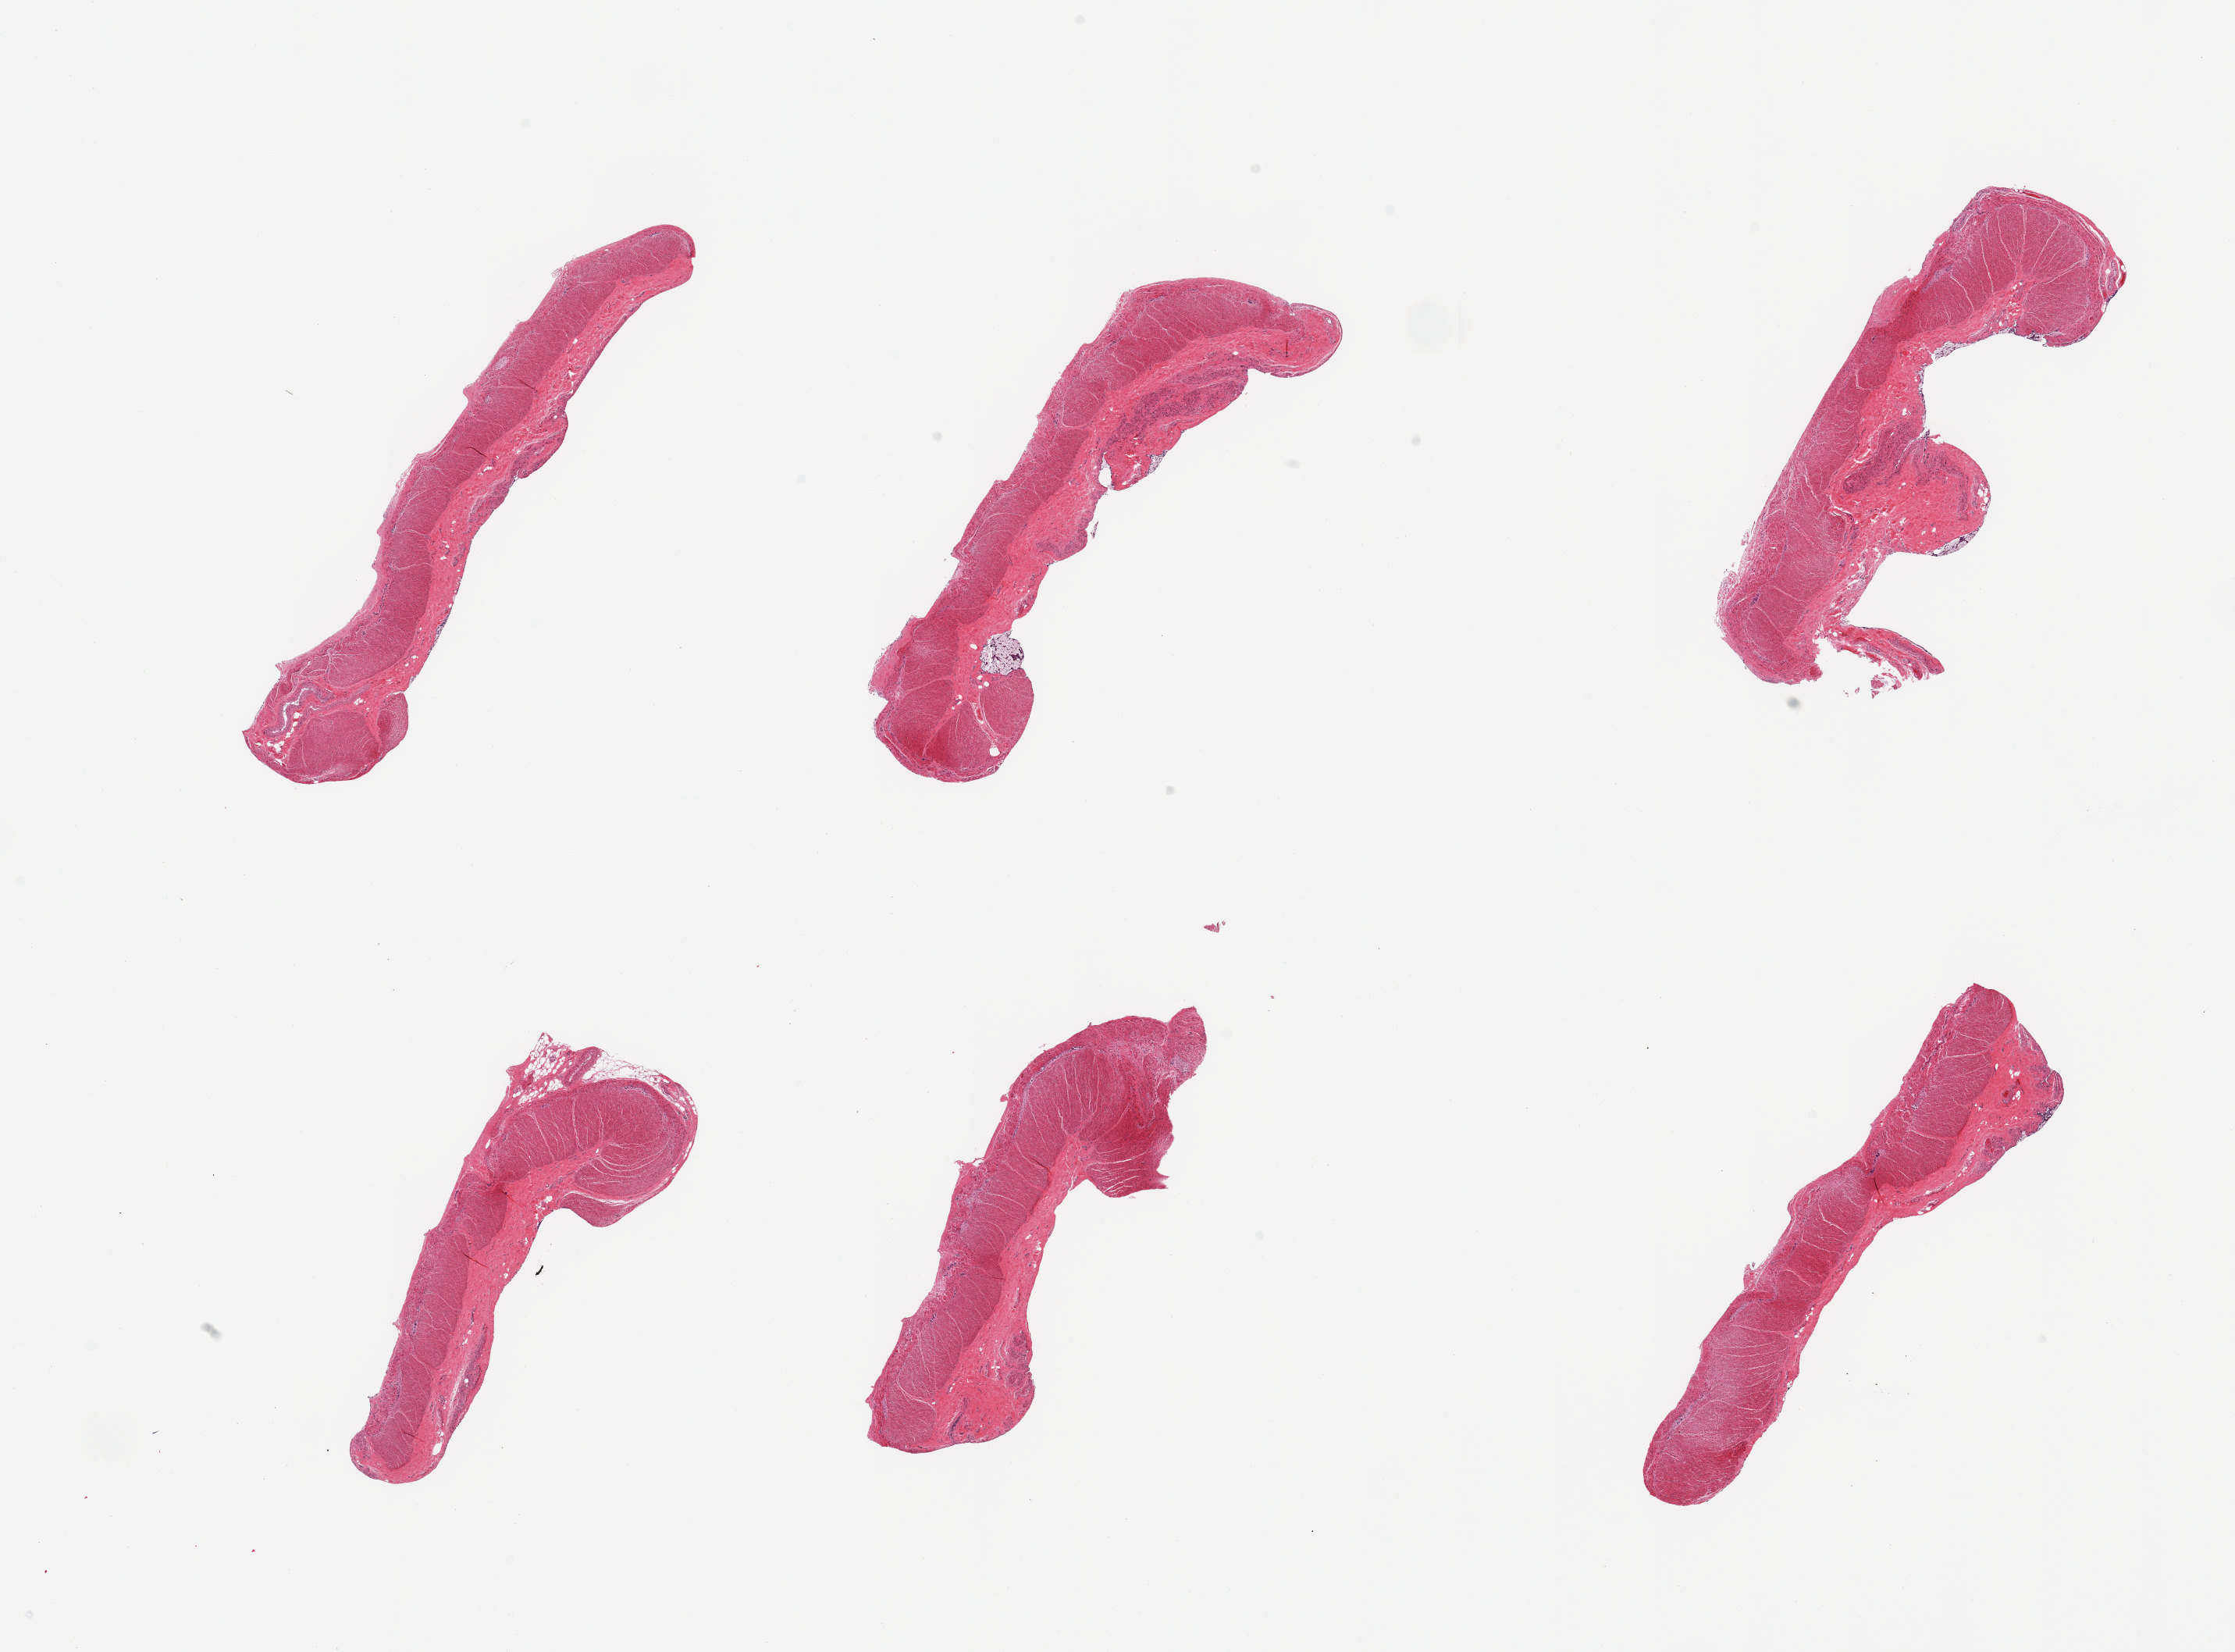
Whole-slide image, haematoxylin and eosin stain, whole scanned area (about 22.6 x 16.7 mm) shown as a low-resolution overview. PAXgene-fixed, paraffin-embedded tissue. Target tissue: sigmoid colon. Donor tissue sample. Female donor.
Reviewer comment on this tissue sample: 6 pieces;ell dissected.